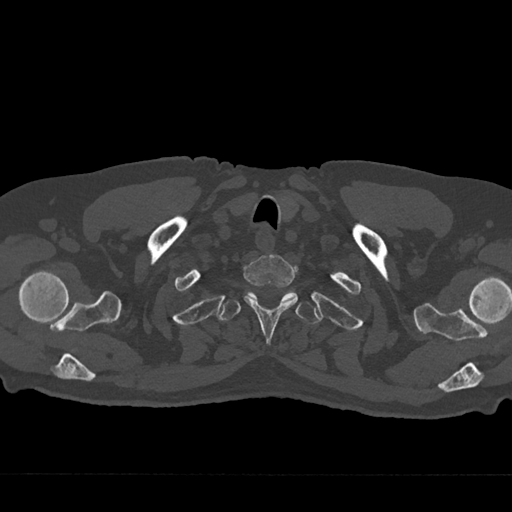
CT including the spine, one axial slice. Slice 642 of 797 in the series (ordered by position). Reconstruction kernel Br40s/3. Bone window (W 1800 / L 400 HU). 512 × 512 image matrix, field of view 377 × 377 mm. Patient: male, 75 years. Case-level facts recorded for this patient, not image findings: primary cancer: renal; vertebrae with lytic lesions (as recorded): T4.
Annotated regions visible in this slice (semi-automatically segmented with operator editing):
- T1 vertebra: bounding box [x1, y1, x2, y2] px = [244, 254, 298, 344]
- T2 vertebra: [218, 290, 320, 324]